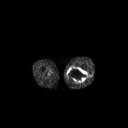
FDG PET of an extremity soft-tissue mass (from a PET/CT study), one axial slice; position 229 of 267 along the scan axis; 3.27 mm slice thickness; 128 × 128 image matrix, field of view 700 × 700 mm. Male patient, age 44 years. From the clinical record (not read from this slice): histological type: undifferentiated pleomorphic liposarcoma; grade: high; site of the primary tumour: left thigh.
Annotated regions visible in this slice (expert contour drawn on MRI and transferred to this co-registered scan by the dataset authors):
- gross tumour volume including surrounding oedema: bounding box [x1, y1, x2, y2] px = [67, 67, 87, 83]
- gross tumour volume (mass): [67, 67, 87, 83]